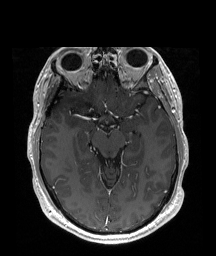
Brain MRI from a brain-tumour surgery series, one axial slice. Position 117 of 192 along the scan axis. T1-weighted post-contrast. 216 × 256 image matrix. From the clinical record (not read from this slice): histopathology: Astrocytoma; WHO grade: 2; IDH mutation: yes; tumour location: Right Insular.
Structures marked on this image (expert manual segmentation):
- tumour: box from (x=67, y=97) to (x=90, y=129) px